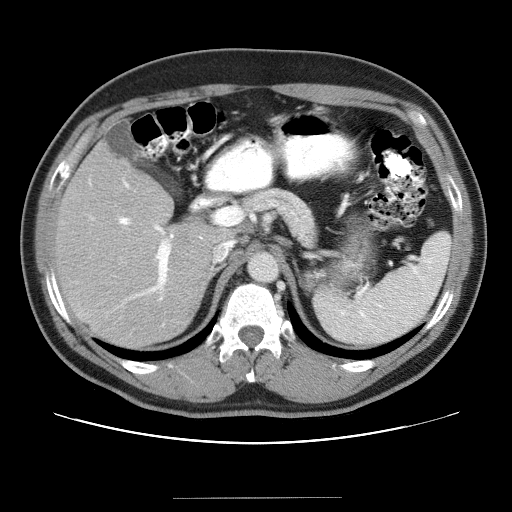
Contrast-enhanced abdominal CT (liver protocol), one axial slice; slice 20 of 40 in the series (ordered by position); reconstruction kernel STANDARD; 120 kVp; soft-tissue window (W 400 / L 40 HU); 5 mm slice thickness; 512 × 512 image matrix, field of view 380 × 380 mm. From the clinical record (not read from this slice): diagnosis: hepatocellular carcinoma (patient treated with transarterial chemoembolisation; whether this scan precedes or follows treatment is not stated here); TNM stage (as recorded): Stage-IVA; Child-Pugh class: B; tumour nodularity: multinodular.
Structures marked on this image (semi-automatic segmentation, software-assisted and operator-edited):
- liver parenchyma outside the tumour (the mass and vessels are separate outlines, so this box may not span the whole liver): bounding box <54,140,222,346> (left, top, right, bottom; pixels)
- liver vessels: <89,179,202,300>